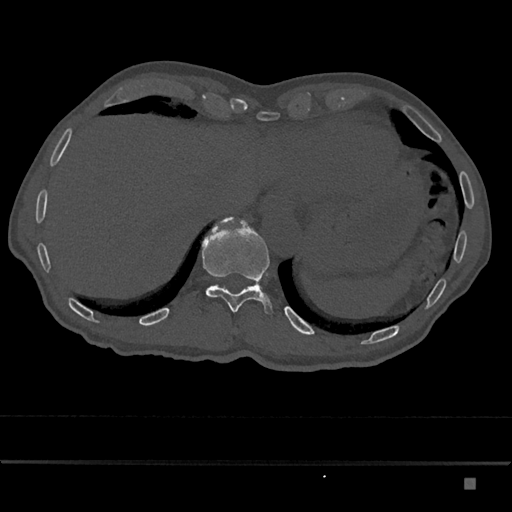
CT including the spine, one axial slice. Slice 676 of 797 in the series (ordered by position). 120 kVp. Bone window (W 1800 / L 400 HU). 512 × 512 image matrix, field of view 390 × 390 mm. Patient: male, 72 years. Case-level facts recorded for this patient, not image findings: primary cancer: prostate.
Annotated regions visible in this slice (semi-automatic segmentation, software-assisted and operator-edited):
- T11 vertebra: bounding box [x1, y1, x2, y2] px = [202, 216, 274, 314]